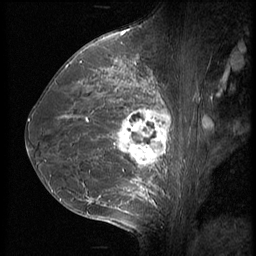
Breast MRI (dynamic contrast-enhanced), one sagittal slice. Position 33 of 56 along the scan axis. 3 images stored at this slice position (order not interpretable as contrast timing). 1.5 T. TE 4.2 ms, TR 9 ms. 2.5 mm slice thickness. 256 × 256 image matrix, field of view 180 × 180 mm. Female patient, age 35 years. Case-level facts recorded for this patient, not image findings: setting: breast cancer imaged before/during neoadjuvant chemotherapy; receptor status: HR-positive, HER2-negative.
Annotated regions visible in this slice (semi-automatic segmentation, software-assisted and operator-edited):
- analysis volume of interest (the breast-tissue region the enhancement analysis was run in; not a lesion): box from (x=63, y=60) to (x=190, y=218) px
- tumour enhancement mask (voxels above the 140 % enhancement threshold inside the analysis volume of interest): (x=89, y=76)–(x=171, y=203)